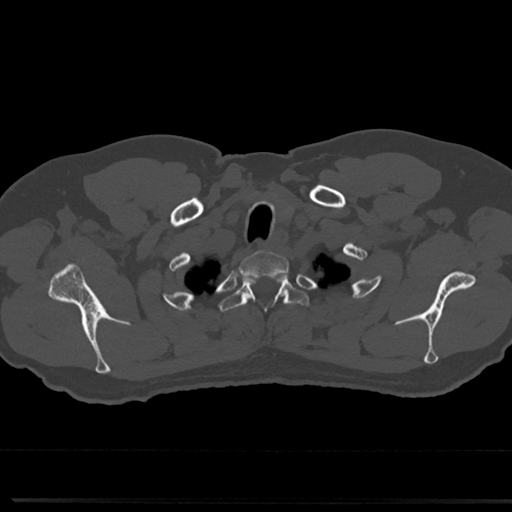
CT including the spine, one axial slice. Position 647 of 817 along the scan axis. Reconstruction kernel Br40s/3. 120 kVp. Bone window (W 1800 / L 400 HU). 0.5 mm slice thickness. 512 × 512 image matrix, field of view 355 × 355 mm. Patient: male, 61 years. Case-level facts recorded for this patient, not image findings: primary cancer: prostate.
Annotated regions visible in this slice (semi-automatically segmented with operator editing):
- T1 vertebra: box from (x=242, y=251) to (x=287, y=267) px
- T2 vertebra: (x=225, y=273)–(x=305, y=325)